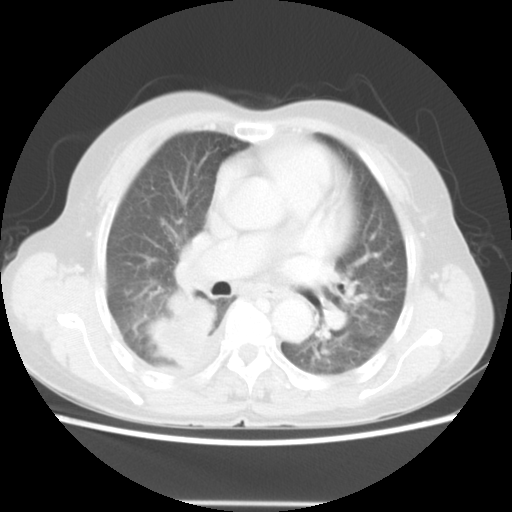
Chest CT, one axial slice; position 29 of 52 along the scan axis; 140 kVp; lung window (W 1500 / L -600 HU); 5 mm slice thickness; 512 × 512 image matrix. Female patient, age 67 years. From the clinical record (not read from this slice): clinical TNM (as recorded): T3 N1 M1.
Structures marked on this image (rectangle marked by the reading radiologist):
- lung tumour (recorded histology: adenocarcinoma): box from (x=143, y=287) to (x=219, y=373) px